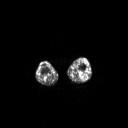
FDG PET of an extremity soft-tissue mass (from a PET/CT study), one axial slice; position 195 of 267 along the scan axis; 3.27 mm slice thickness; 128 × 128 image matrix, field of view 700 × 700 mm. Male patient, age 44 years. From the clinical record (not read from this slice): histological type: undifferentiated pleomorphic liposarcoma; grade: high; site of the primary tumour: left thigh.
Structures marked on this image (expert contour drawn on MRI and transferred to this co-registered scan by the dataset authors):
- gross tumour volume including surrounding oedema: bounding box [x1, y1, x2, y2] px = [71, 71, 75, 75]